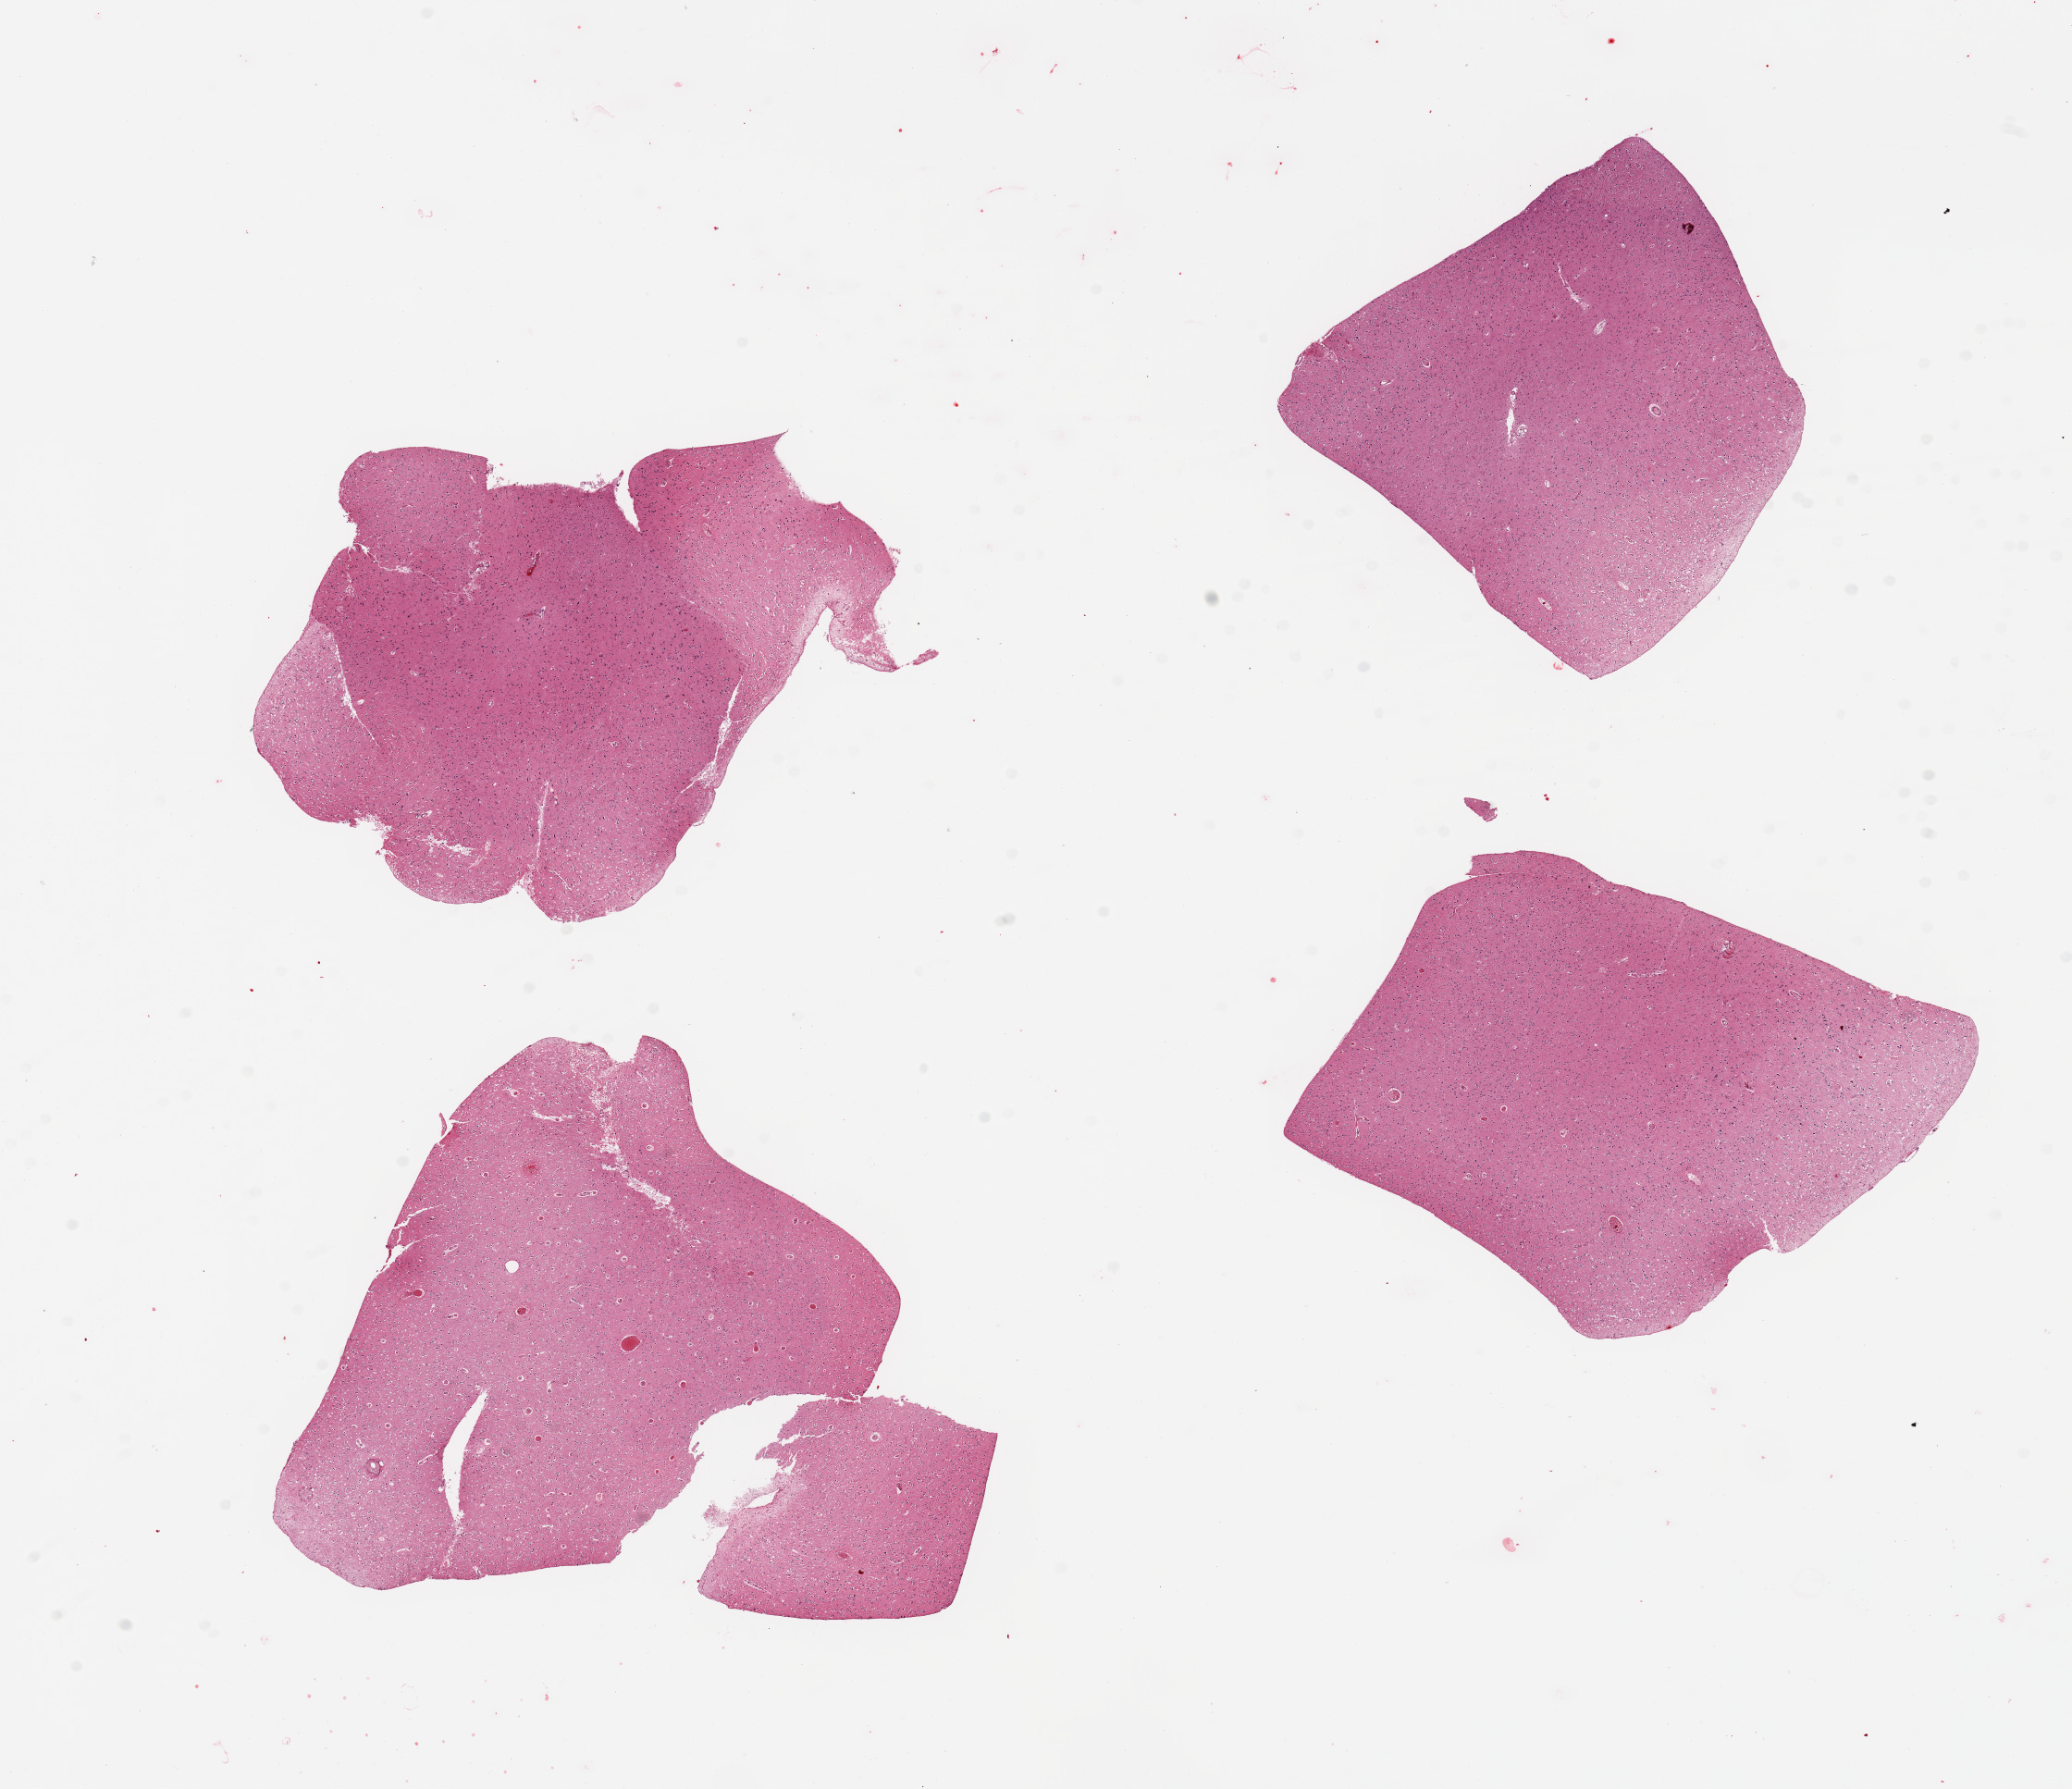
Digitized H&E-stained section — a low-resolution overview of the entire scanned area, about 17.7 x 15.3 mm (acquisition: 20x scan); PAXgene-fixed, paraffin-embedded tissue; target tissue: cerebral cortex; tissue donor sample. Donor sex: female.
Review note (as recorded): 4 pieces, no abnormalities.